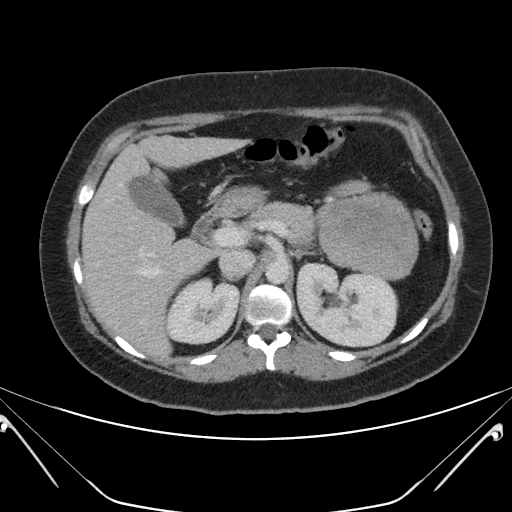
Contrast-enhanced abdominal CT, one axial slice. 120 kVp. Intravenous contrast given. Soft-tissue window (W 400 / L 40 HU). 512 × 512 image matrix, field of view 394 × 394 mm. Patient: female, 26 years. From the clinical record (not read from this slice): diagnosis: adrenocortical carcinoma; tumour side: left adrenal; tumour size at pathology: 28 cm; Ki-67 index: 20 %; stage (as recorded): 2.
Structures marked on this image (semi-automatic segmentation, software-assisted and operator-edited):
- mass: bounding box <319,195,416,279> (left, top, right, bottom; pixels)